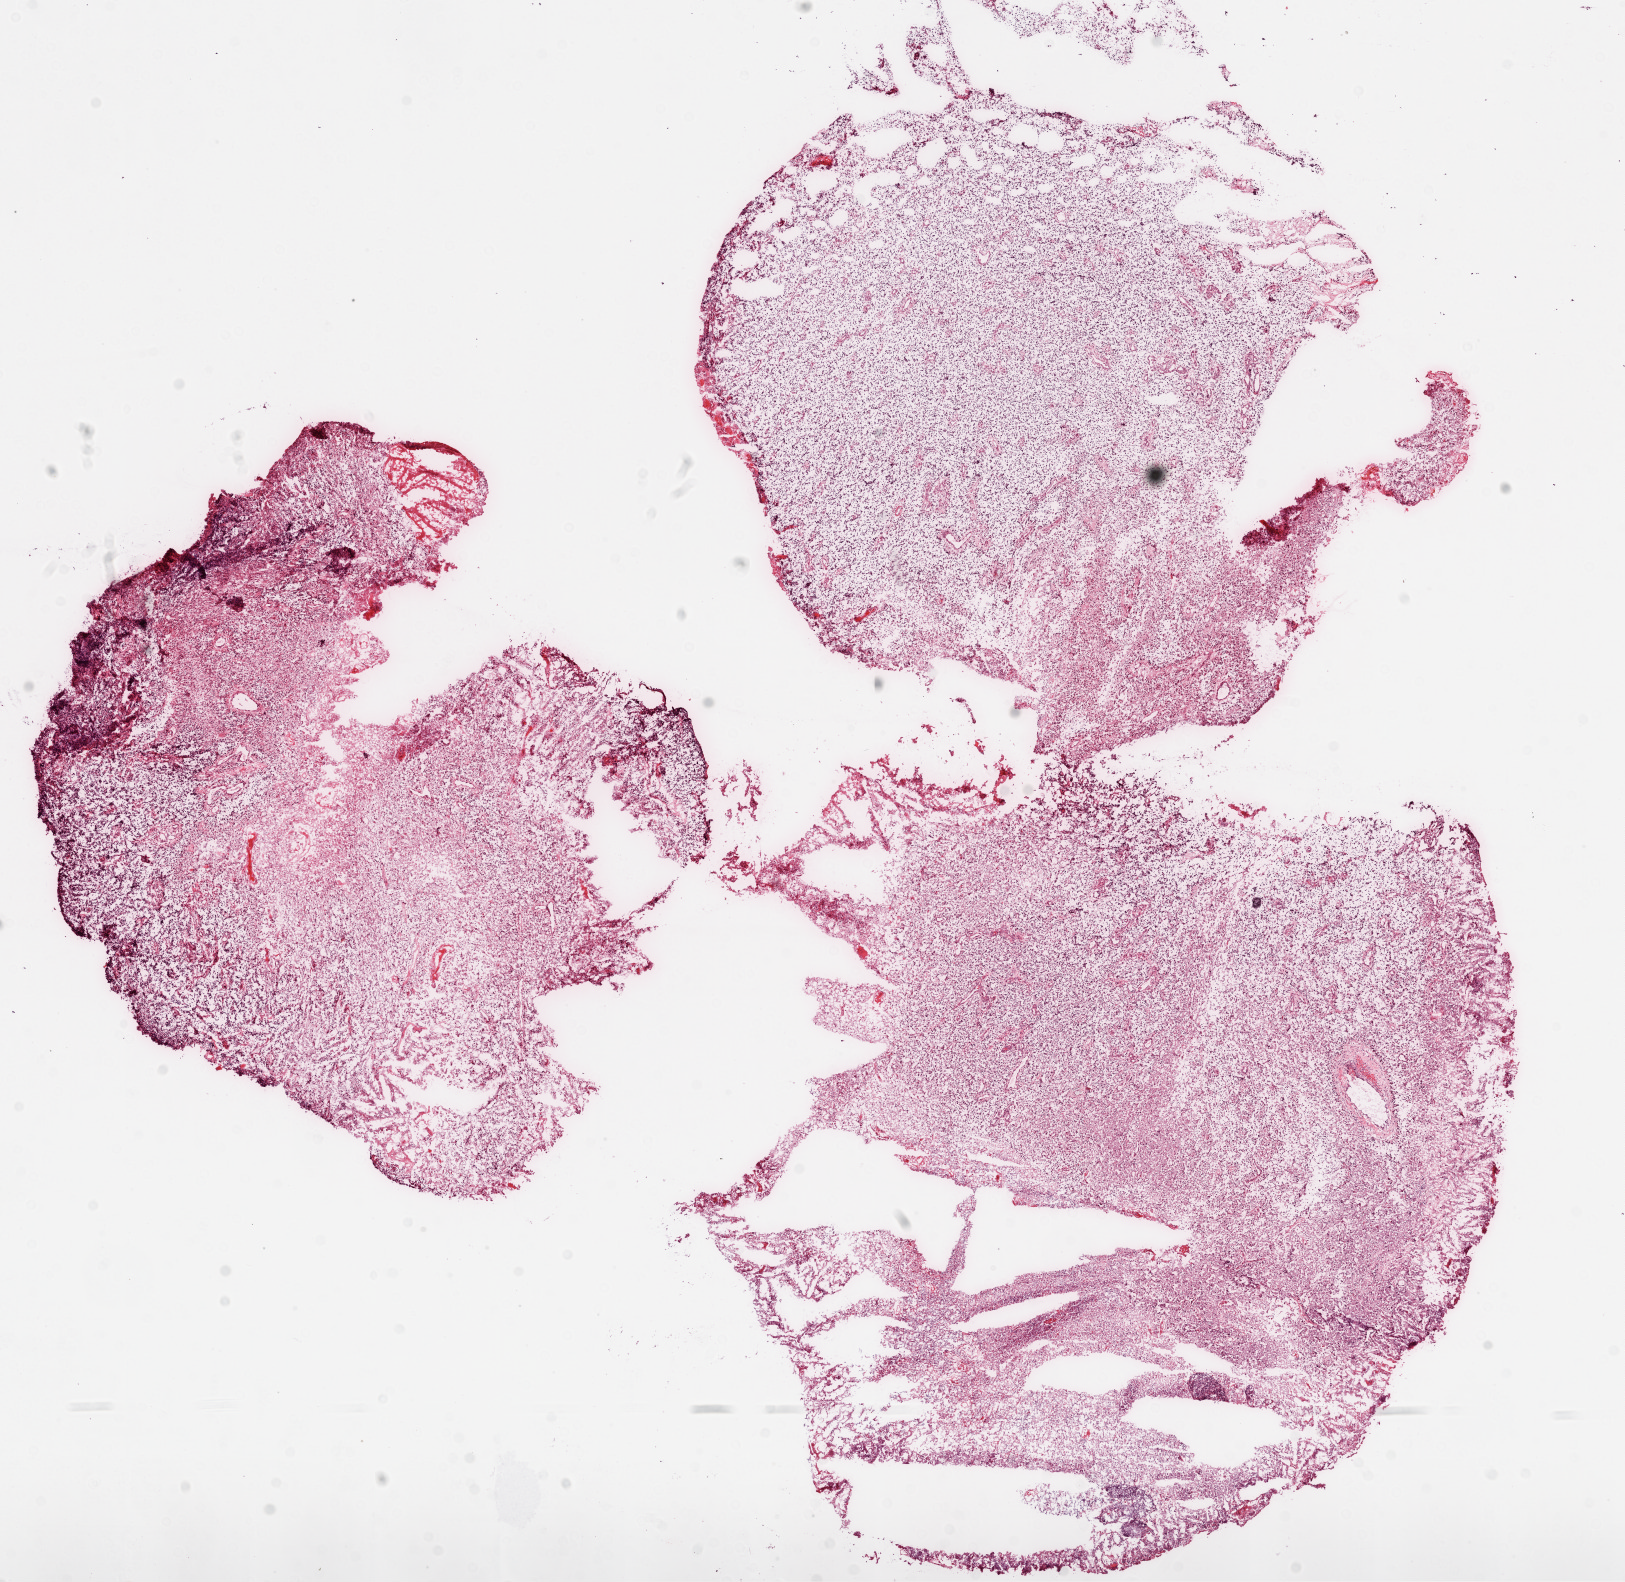
Digitized H&E-stained tissue section (whole slide), shown as a low-resolution overview of the whole scanned area (about 13.0 x 12.7 mm). Frozen section from the top of the tissue portion. Sample: primary tumour, brain. Patient: male, age at initial diagnosis 61 years. Composition of this section per pathologist review: tumour cells 85%, tumour nuclei 100%, normal cells 0%, stromal cells 0%, necrosis 15%.
Diagnosis: Glioblastoma.